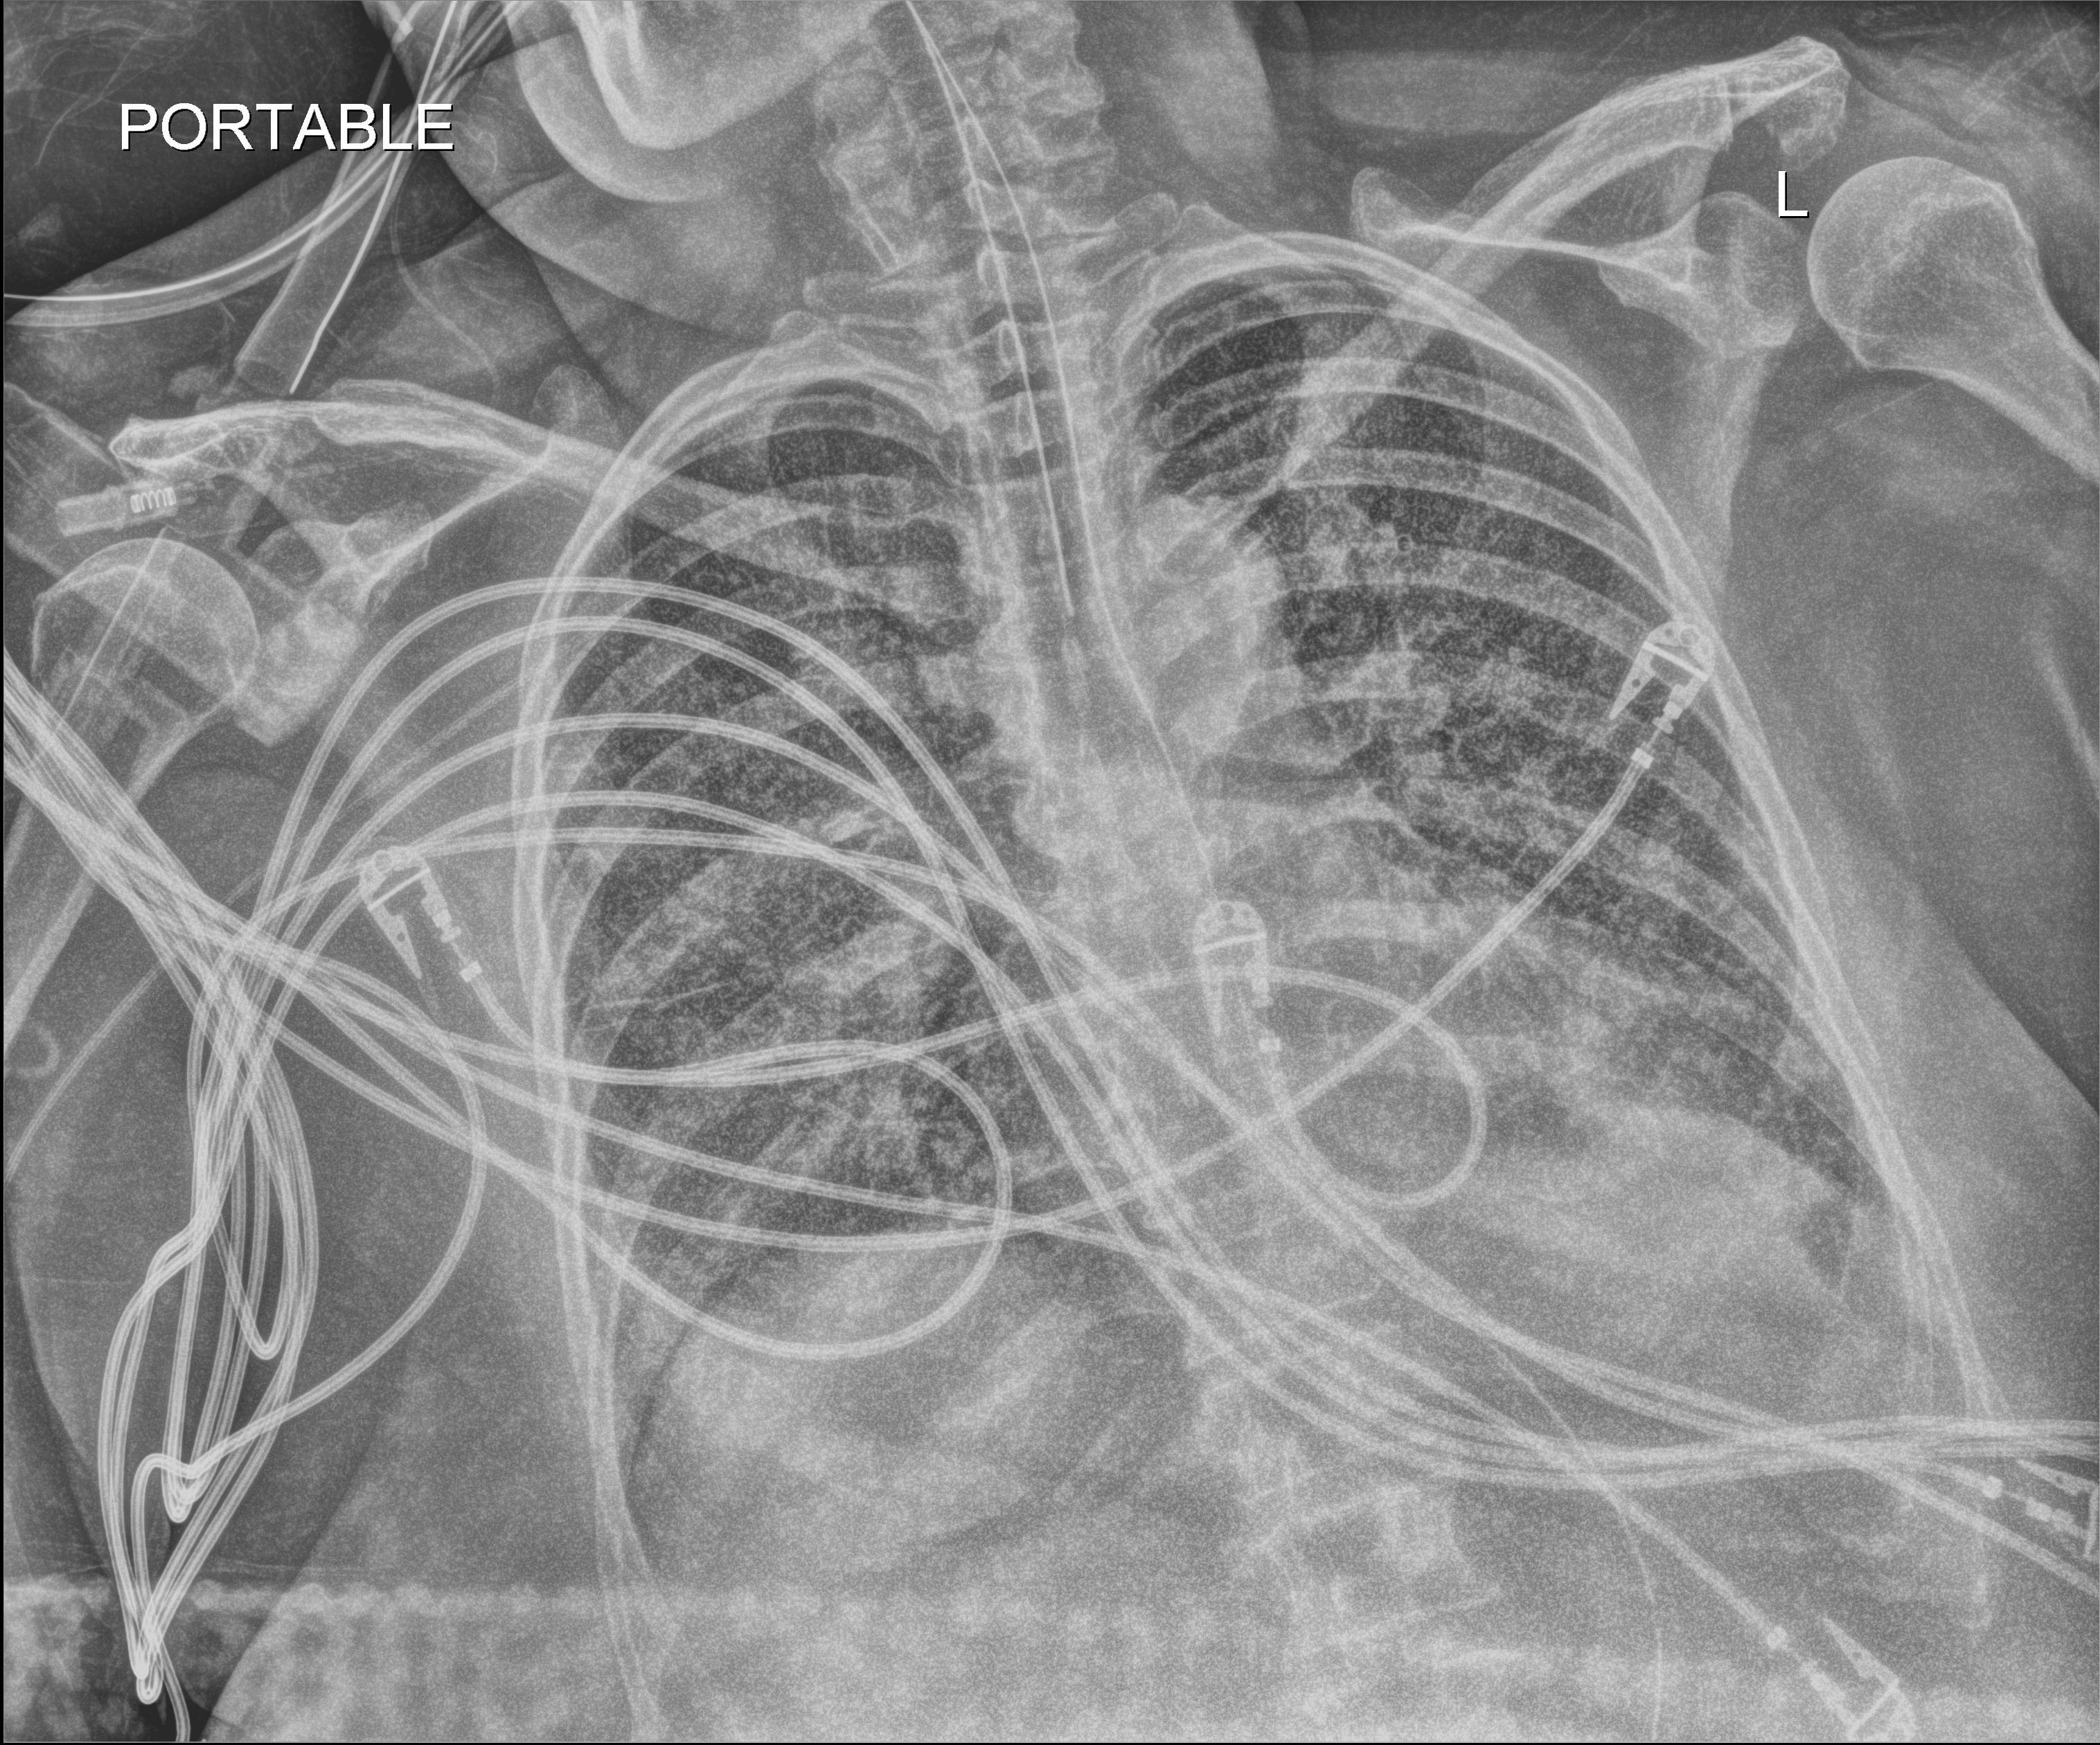
Bedside chest radiograph (digital radiography), anteroposterior (AP) projection. Patient hospitalised with COVID-19; female, aged 60–74 years.
From the hospital-stay record, not from the radiograph (when in the stay this image was taken is not recorded): other chronic lung disease (admission record): no; mechanically ventilated during this hospital stay: yes; admitted to intensive care during this hospital stay: yes.